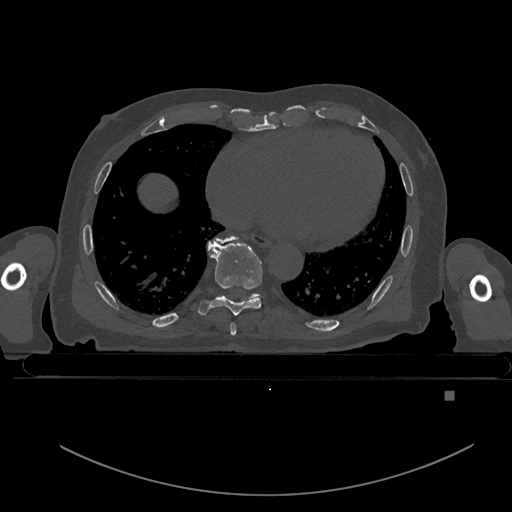
CT including the spine, one axial slice; position 196 of 969 along the scan axis; bone window (W 1800 / L 400 HU); 512 × 512 image matrix, field of view 456 × 456 mm. Patient: male, 82 years. From the clinical record (not read from this slice): primary cancer: prostate.
Outlined on this slice (semi-automatic segmentation, software-assisted and operator-edited):
- T7 vertebra: box from (x=230, y=322) to (x=236, y=336) px
- T8 vertebra: (x=198, y=237)–(x=268, y=316)
- T9 vertebra: (x=216, y=236)–(x=260, y=299)